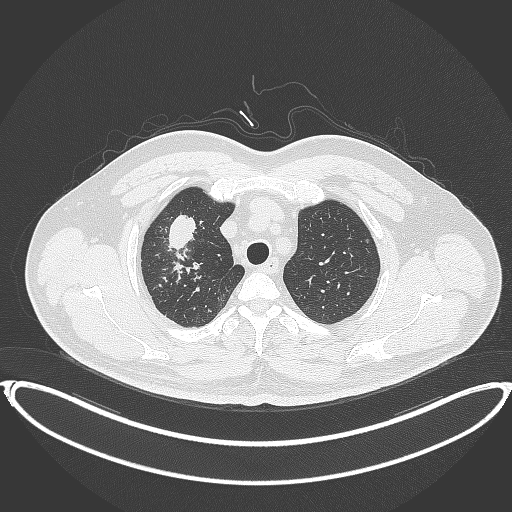
Chest CT, one axial slice; reconstruction kernel B70f; lung window (W 1500 / L -600 HU); 1 mm slice thickness; 512 × 512 image matrix. Male patient, age 53 years. Case-level facts recorded for this patient, not image findings: clinical TNM (as recorded): T2a N0 M0.
Annotated regions visible in this slice (bounding box drawn by a radiologist):
- lung tumour (recorded histology: adenocarcinoma): bounding box [x1, y1, x2, y2] px = [165, 215, 200, 259]